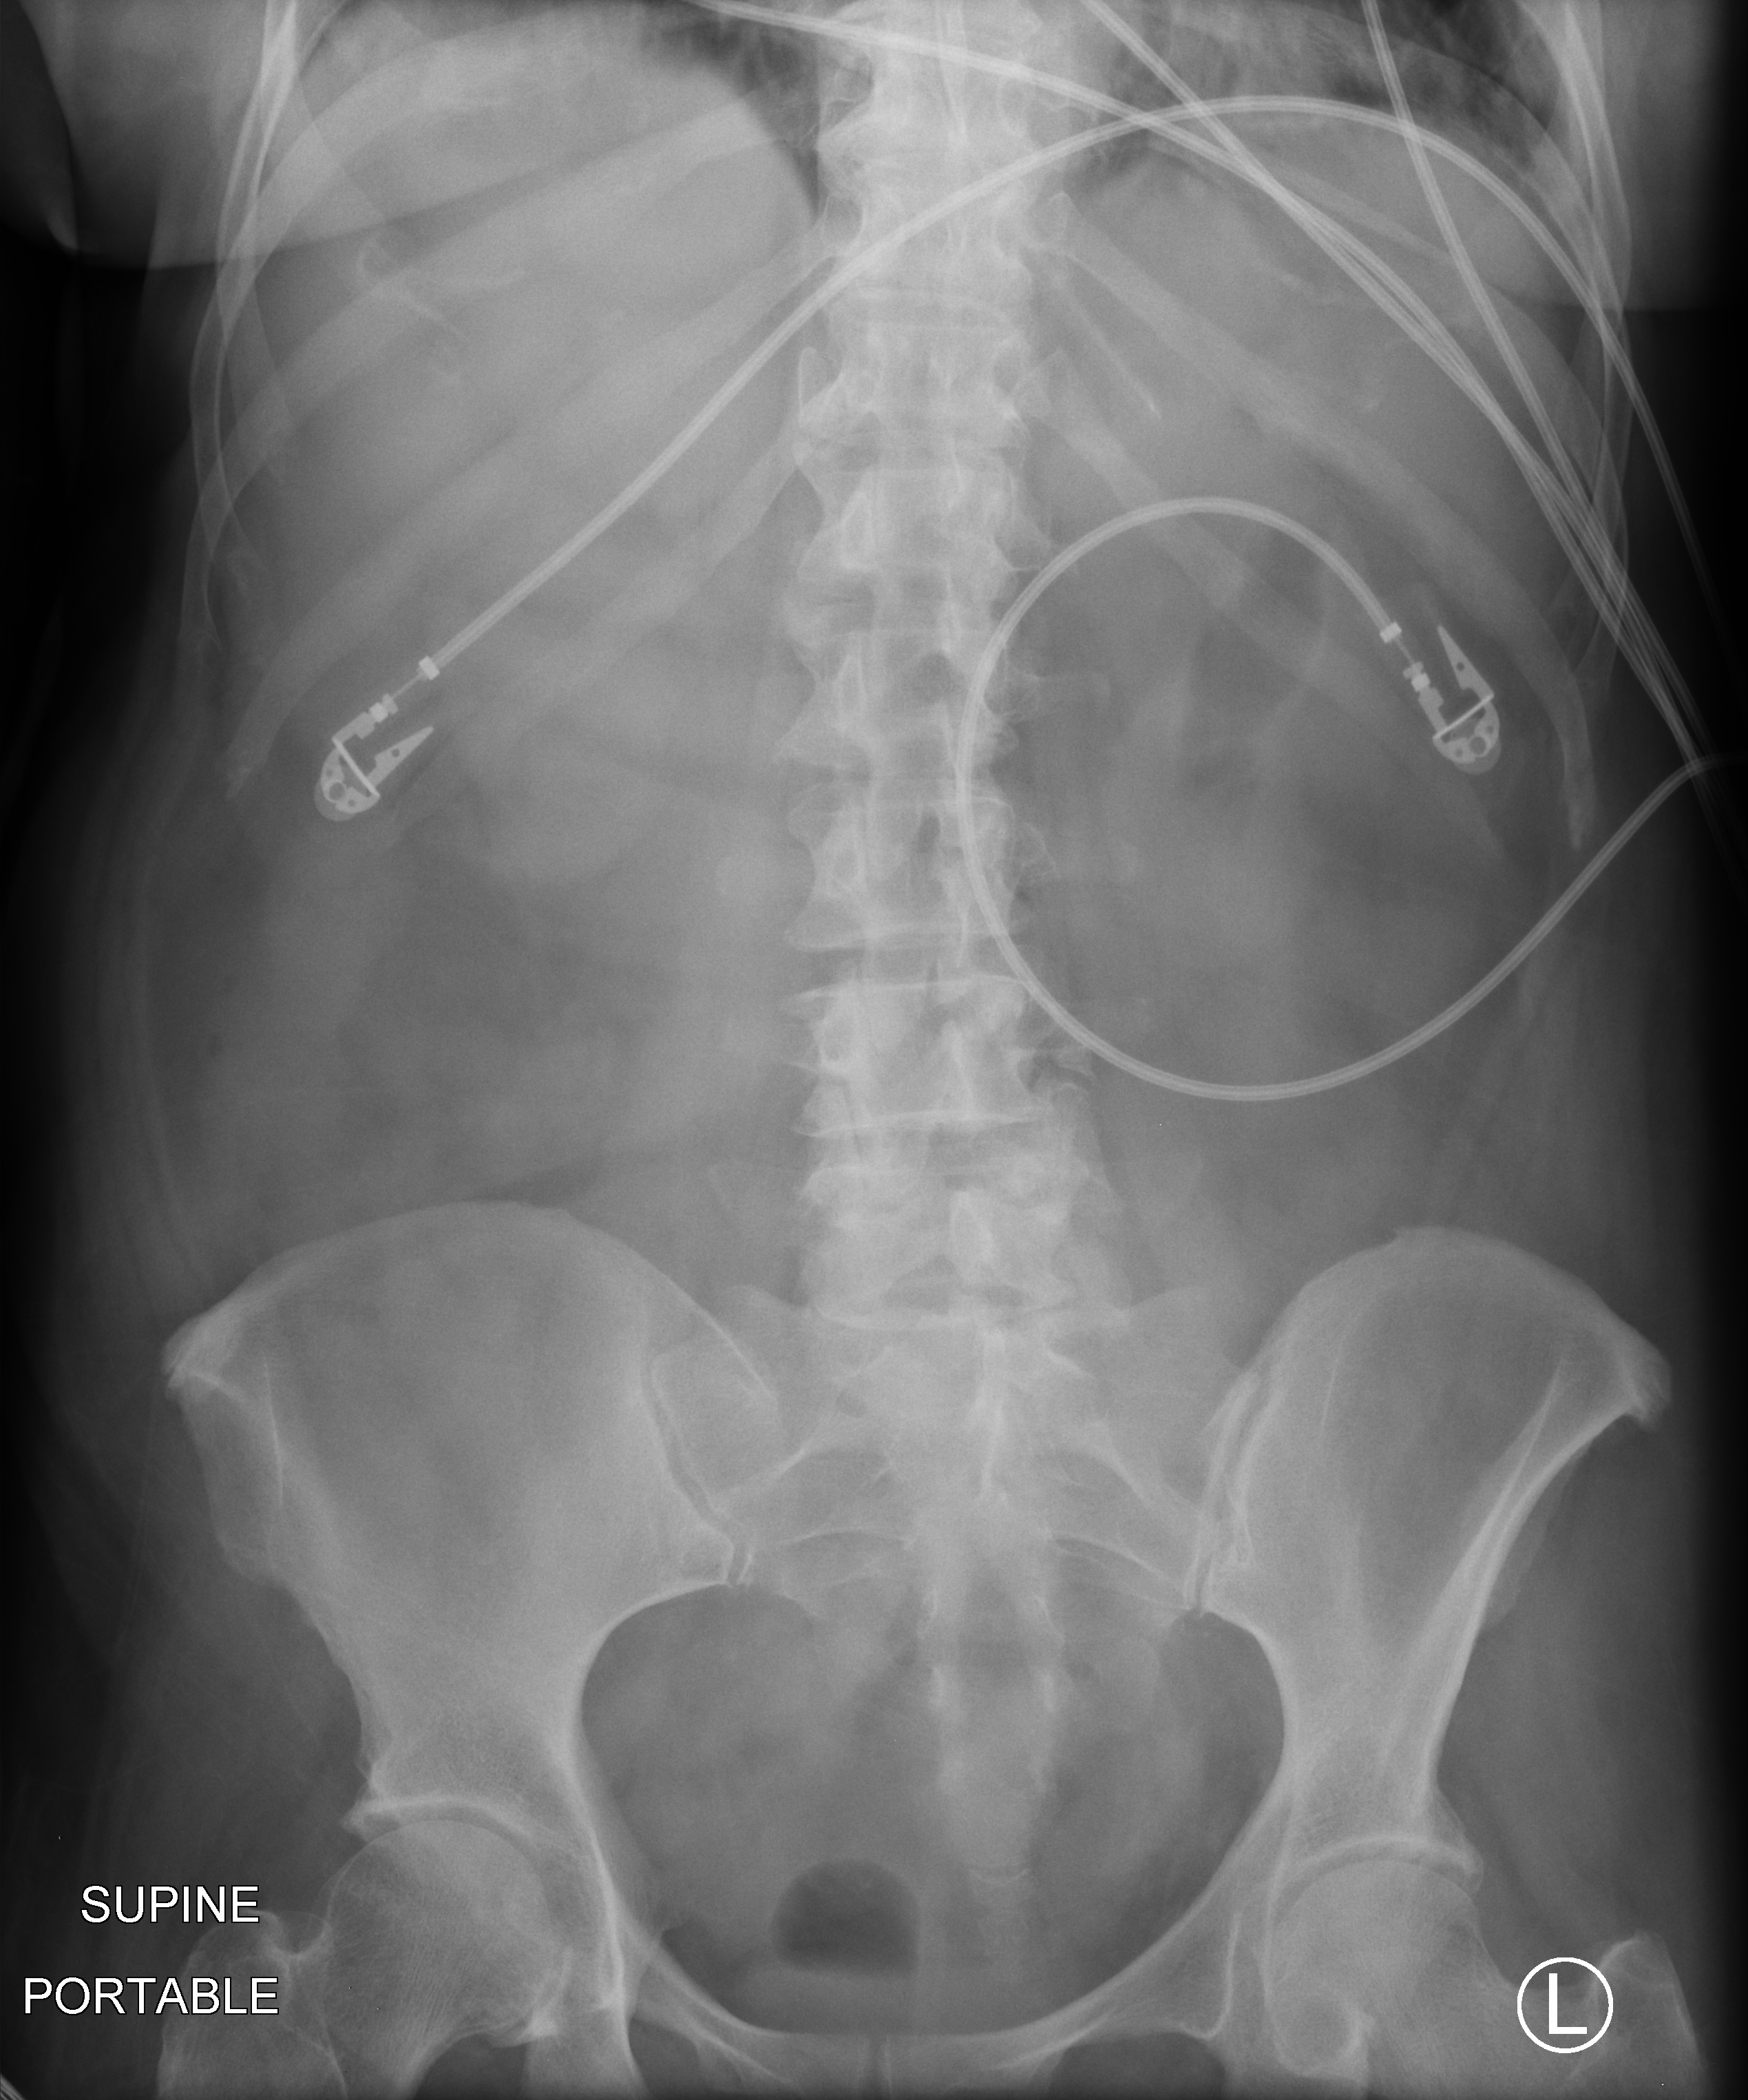
Portable abdomen radiograph, anteroposterior (AP) projection. Female patient hospitalised with COVID-19, age 60–74 years.
Hospital-stay facts (about this admission, not read from this image; timing relative to this image not recorded): mechanically ventilated during this hospital stay: yes.